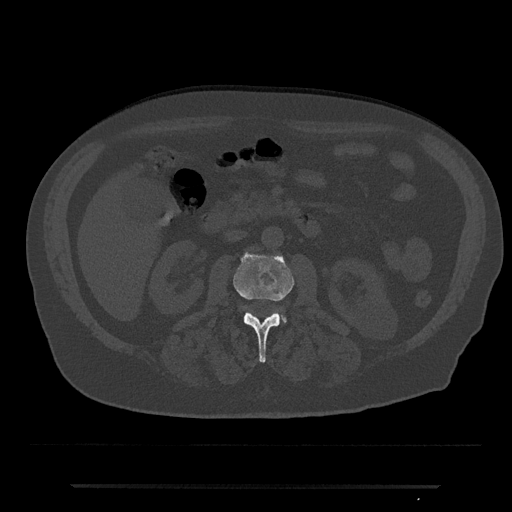
CT including the spine, one axial slice. Slice 457 of 797 in the series (ordered by position). Bone window (W 1800 / L 400 HU). 0.5 mm slice thickness. 512 × 512 image matrix, field of view 434 × 434 mm. Patient: male, 80 years. From the clinical record (not read from this slice): primary cancer: prostate; vertebrae with lytic lesions (as recorded): L1, T11.
Outlined on this slice (semi-automatic segmentation, software-assisted and operator-edited):
- L2 vertebra: box from (x=233, y=253) to (x=294, y=363) px
- L3 vertebra: (x=281, y=315)–(x=287, y=323)